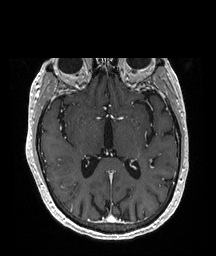
Brain MRI from a brain-tumour surgery series, one axial slice. Slice 111 of 208 in the series (ordered by position). T1-weighted post-contrast. 1 mm slice thickness. 216 × 256 image matrix. Case-level facts recorded for this patient, not image findings: histopathology: Glioblastoma; WHO grade: 4; IDH mutation: no; tumour location: Right Temporal.
Annotated regions visible in this slice (expert manual segmentation):
- tumour: bounding box [x1, y1, x2, y2] px = [65, 182, 72, 188]